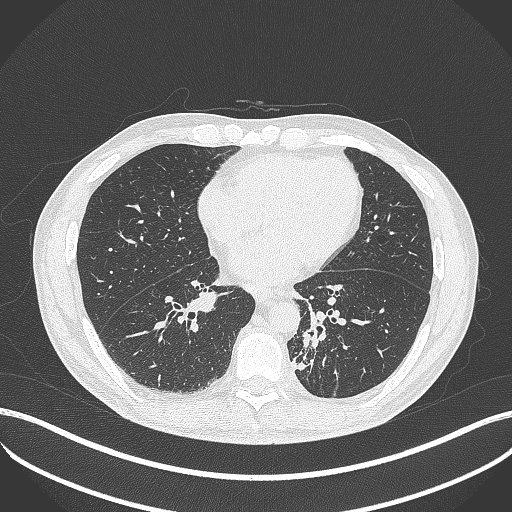
Chest CT, one axial slice. Reconstruction kernel B70f. 120 kVp. Lung window (W 1500 / L -600 HU). 512 × 512 image matrix, field of view 400 × 400 mm. Male patient, age 72 years. Case-level facts recorded for this patient, not image findings: clinical TNM (as recorded): T2b N0 M1.
Structures marked on this image (rectangle marked by the reading radiologist):
- lung tumour (recorded histology: adenocarcinoma): bounding box (x1, y1, x2, y2) in pixels: (293, 331, 325, 375)